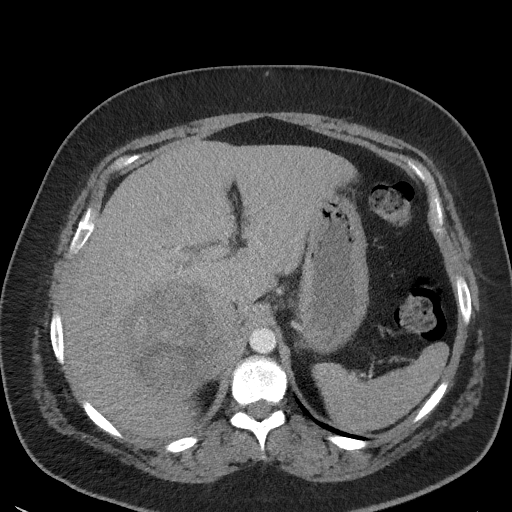
Contrast-enhanced abdominal CT, one axial slice. Position 38 of 56 along the scan axis. Reconstruction kernel I41f/3. Intravenous contrast given. Soft-tissue window (W 400 / L 40 HU). 5 mm slice thickness. 512 × 512 image matrix, field of view 373 × 373 mm. Patient: female, 35 years. From the clinical record (not read from this slice): diagnosis: adrenocortical carcinoma; tumour side: right adrenal; tumour size at pathology: 15 cm; Ki-67 index: 40 %; stage (as recorded): 2.
Outlined on this slice (semi-automatically segmented with operator editing):
- mass: box from (x=128, y=285) to (x=218, y=388) px